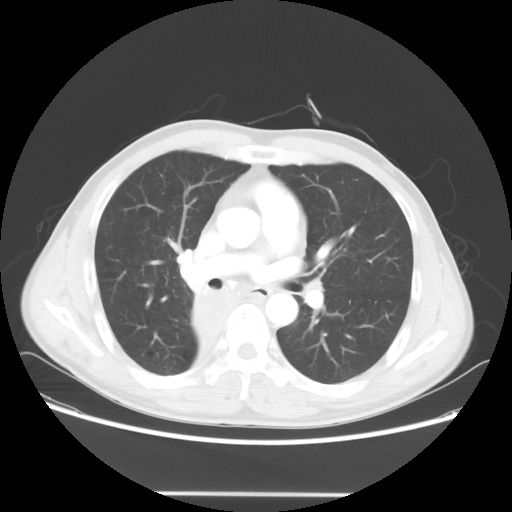
Chest CT, one axial slice. Position 35 of 62 along the scan axis. Reconstruction kernel STANDARD. Lung window (W 1500 / L -600 HU). 5 mm slice thickness. 512 × 512 image matrix. Male patient, age 47 years. Case-level facts recorded for this patient, not image findings: clinical TNM (as recorded): T2 N0 M0.
Outlined on this slice (rectangle marked by the reading radiologist):
- lung tumour (recorded histology: squamous cell carcinoma): box from (x=177, y=282) to (x=231, y=360) px